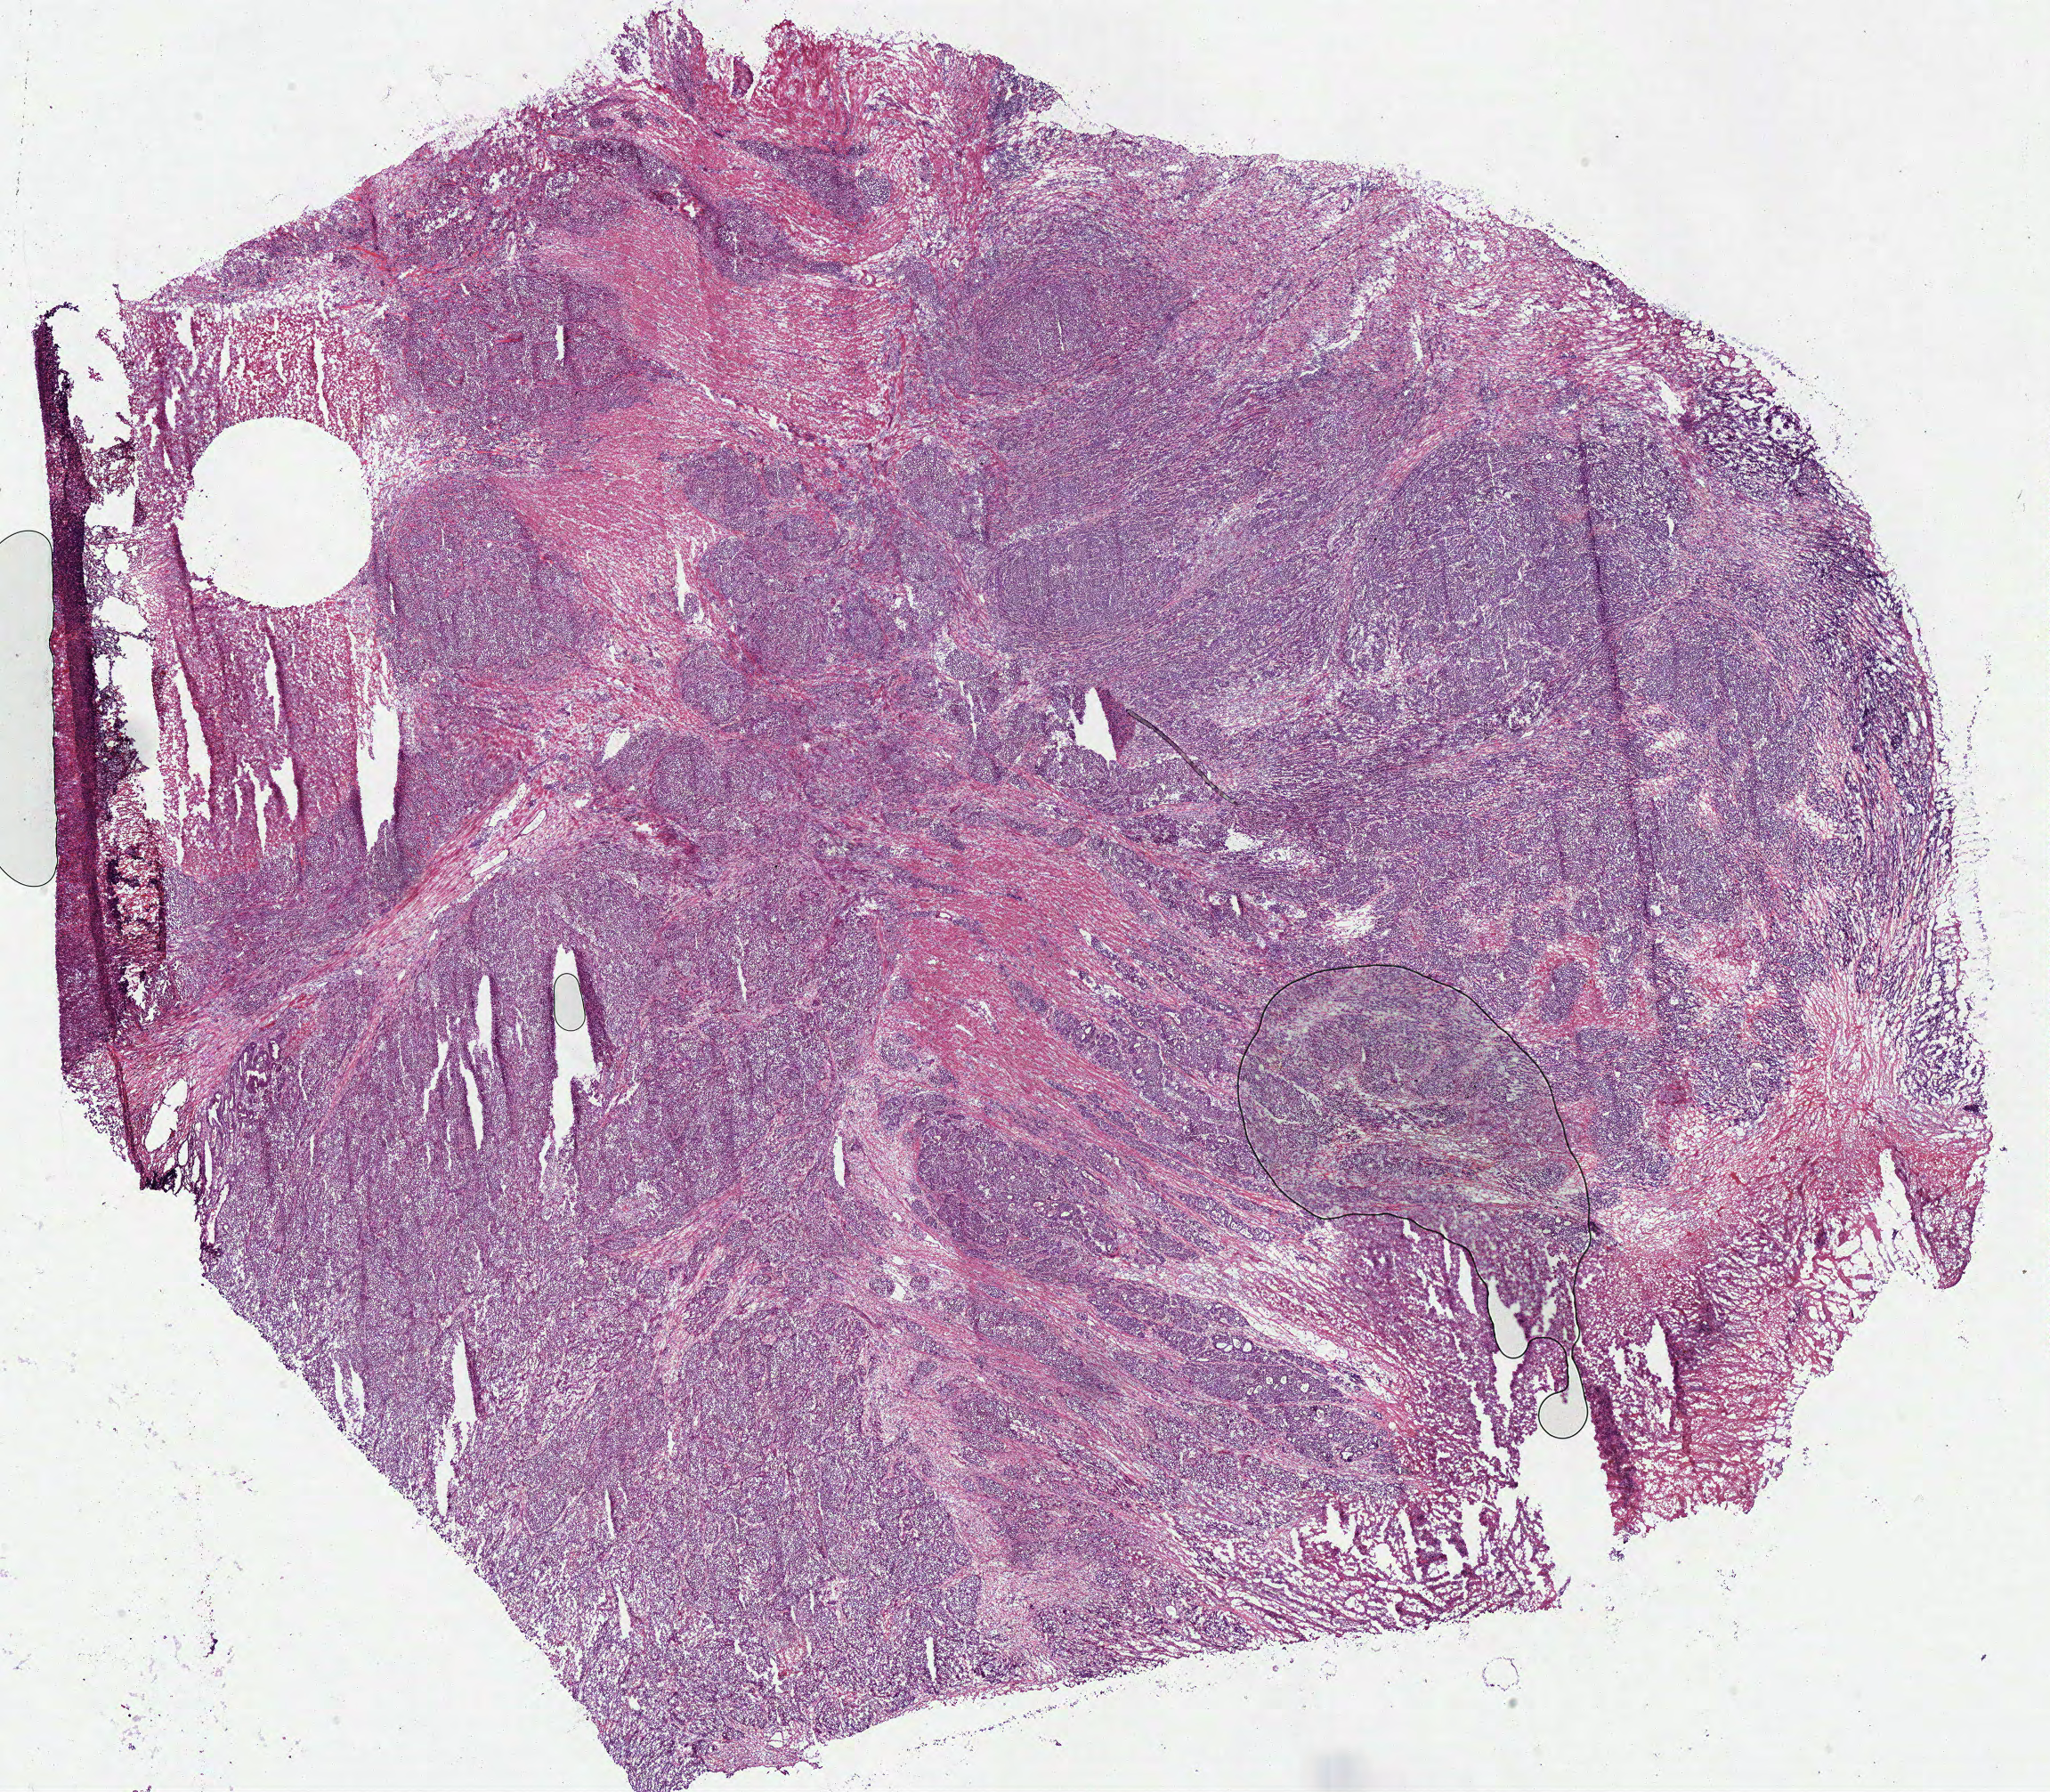
Digitized H&E-stained tissue section (whole slide) — whole scanned area (about 18.1 x 15.8 mm) shown as a low-resolution overview. Frozen section. Primary tumour sample from the colon. Patient: male, age at initial diagnosis 46 years. Composition of this section per pathologist review: tumour cells 73%, tumour nuclei 80%, normal cells 0%, stromal cells 15%, necrosis 12%.
Pathologic diagnosis: Adenocarcinoma, NOS. AJCC pathologic stage: IIA.